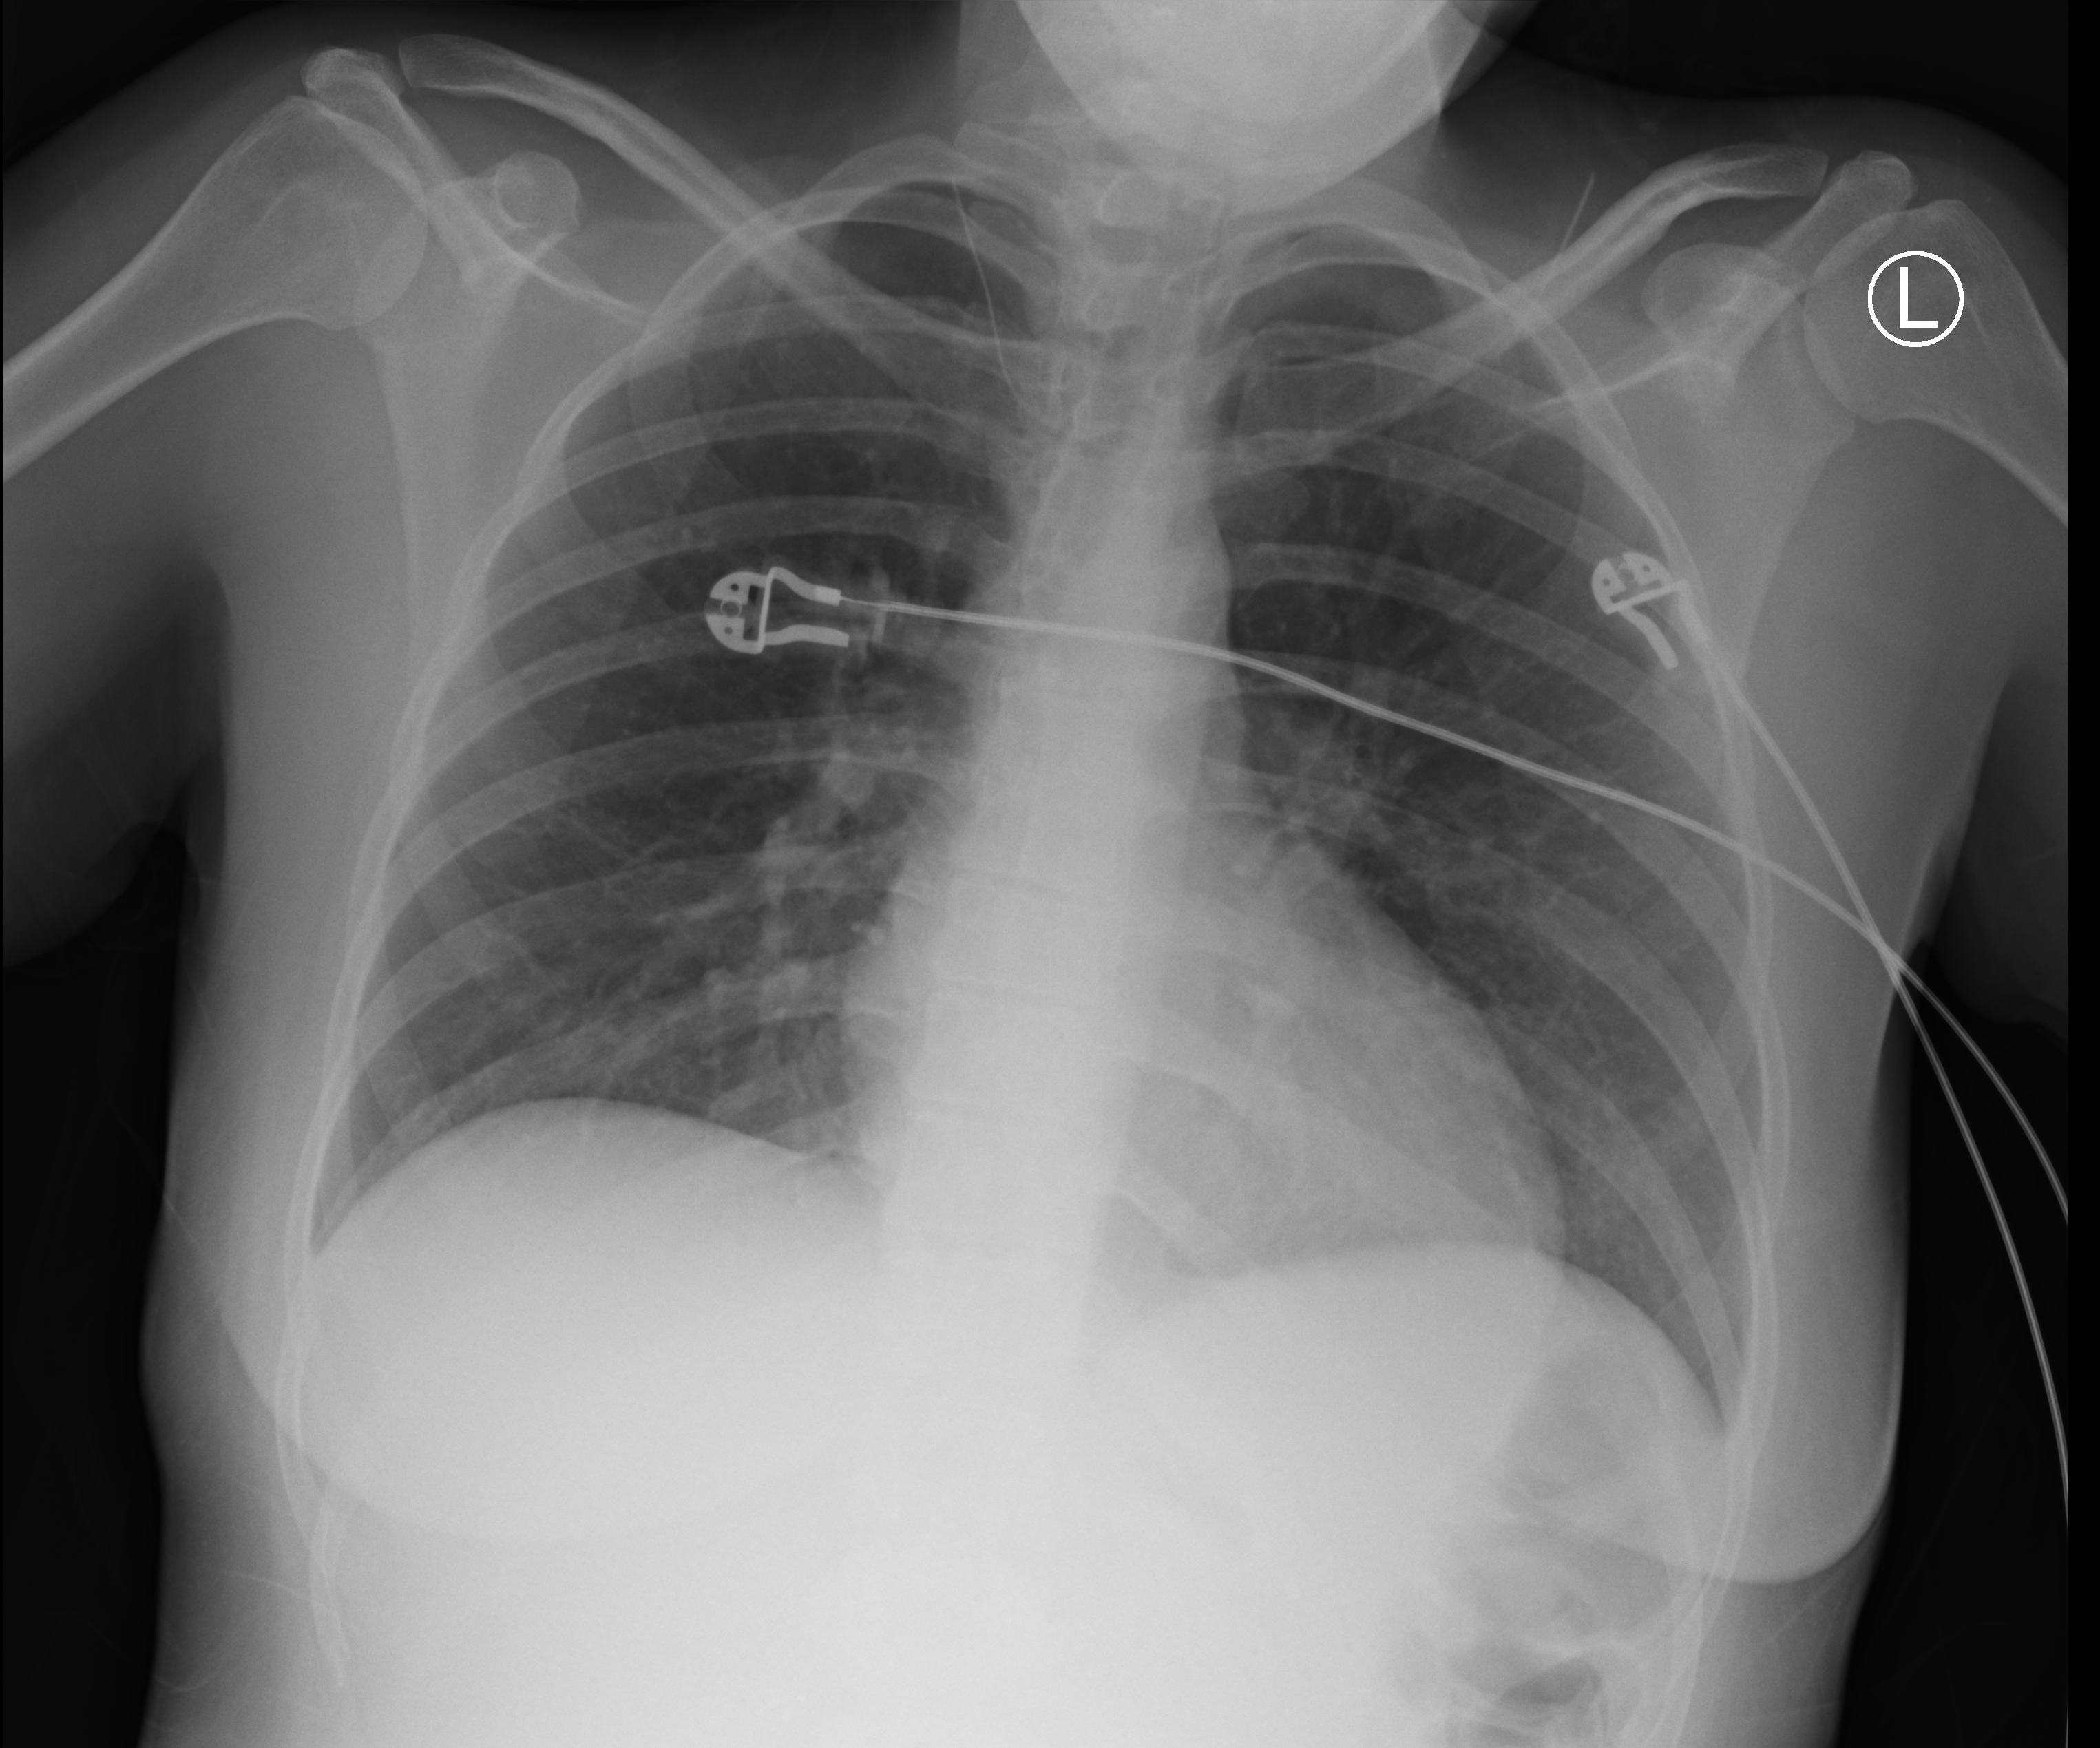
Portable chest radiograph; anteroposterior (AP) projection. Patient hospitalised with COVID-19; female, aged 18–59 years.
From the hospital-stay record, not from the radiograph (when in the stay this image was taken is not recorded):
- mechanically ventilated during this hospital stay: no
- admitted to intensive care during this hospital stay: no